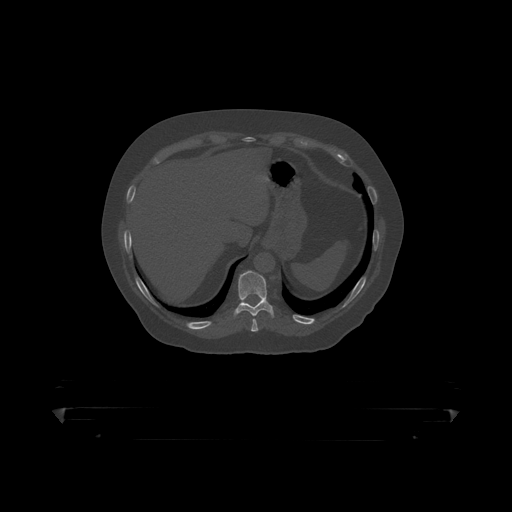
CT including the spine, one axial slice; bone window (W 1800 / L 400 HU); 1.25 mm slice thickness; 512 × 512 image matrix, field of view 650 × 650 mm. Male patient, age 60 years. From the clinical record (not read from this slice): primary cancer: prostate.
Structures marked on this image (semi-automatic segmentation, software-assisted and operator-edited):
- T10 vertebra: bounding box (x1, y1, x2, y2) in pixels: (234, 271, 275, 317)